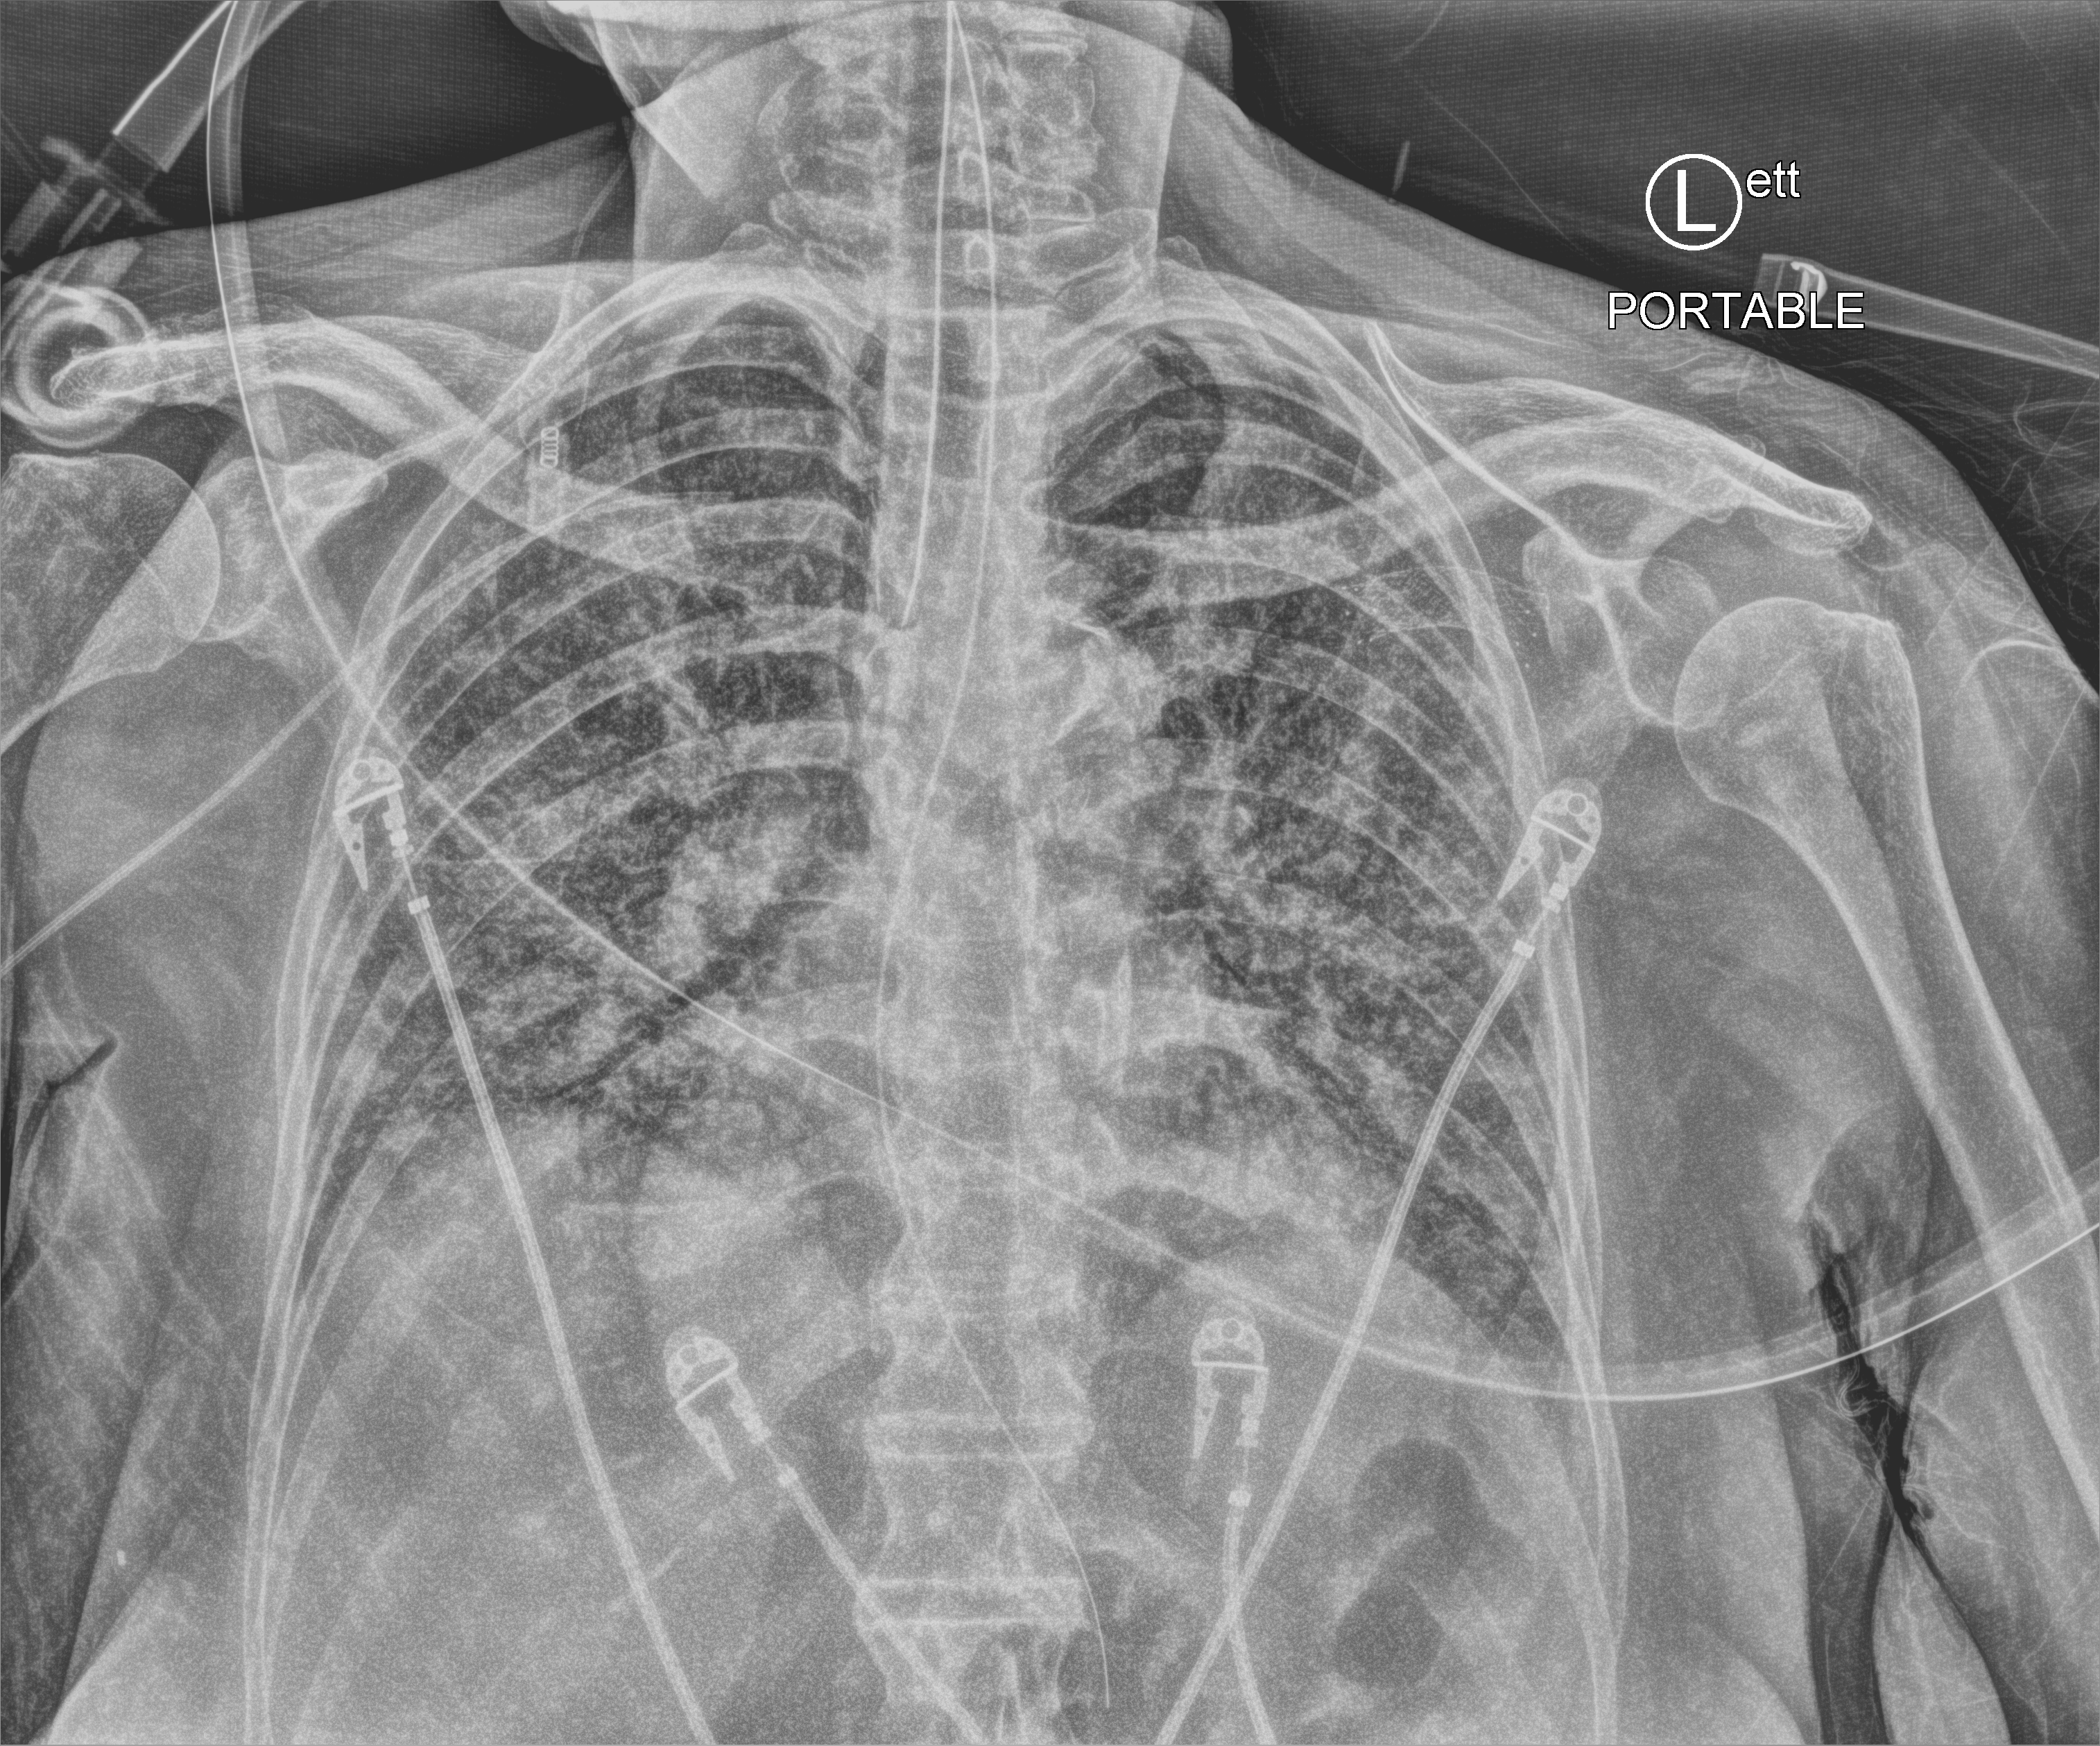
Portable chest radiograph, anteroposterior (AP) projection. Female patient hospitalised with COVID-19, age 60–74 years.
Admission-level facts for this patient (not findings on this image; timing relative to this image not recorded): smoking status (admission record): never; other chronic lung disease (admission record): no.